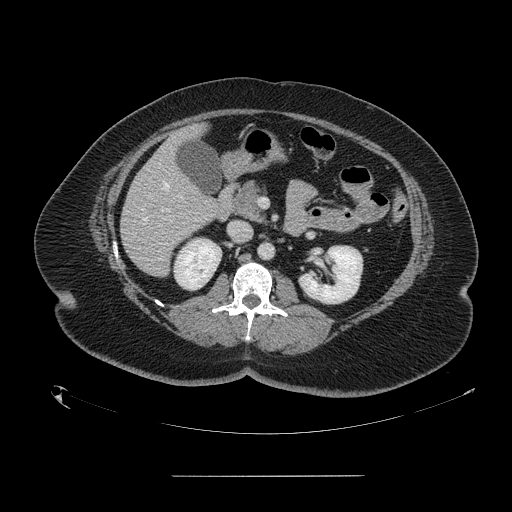
Contrast-enhanced abdominal CT, one axial slice. Position 67 of 164 along the scan axis. 120 kVp. Intravenous contrast given. Soft-tissue window (W 400 / L 40 HU). 2.5 mm slice thickness. 512 × 512 image matrix. Female patient, age 52 years. From the clinical record (not read from this slice): diagnosis: colorectal cancer liver metastases, imaged before liver resection; multiple liver metastases: yes; largest metastasis: 3.5 cm; disease in both lobes: no.
Outlined on this slice (manually delineated by an expert):
- hepatic veins: bounding box <141,183,170,221> (left, top, right, bottom; pixels)
- liver: <122,127,225,276>
- planned liver remnant (the part of the liver to remain after resection): <184,126,205,140>
- portal vein (with intrahepatic branches): <178,195,181,197>